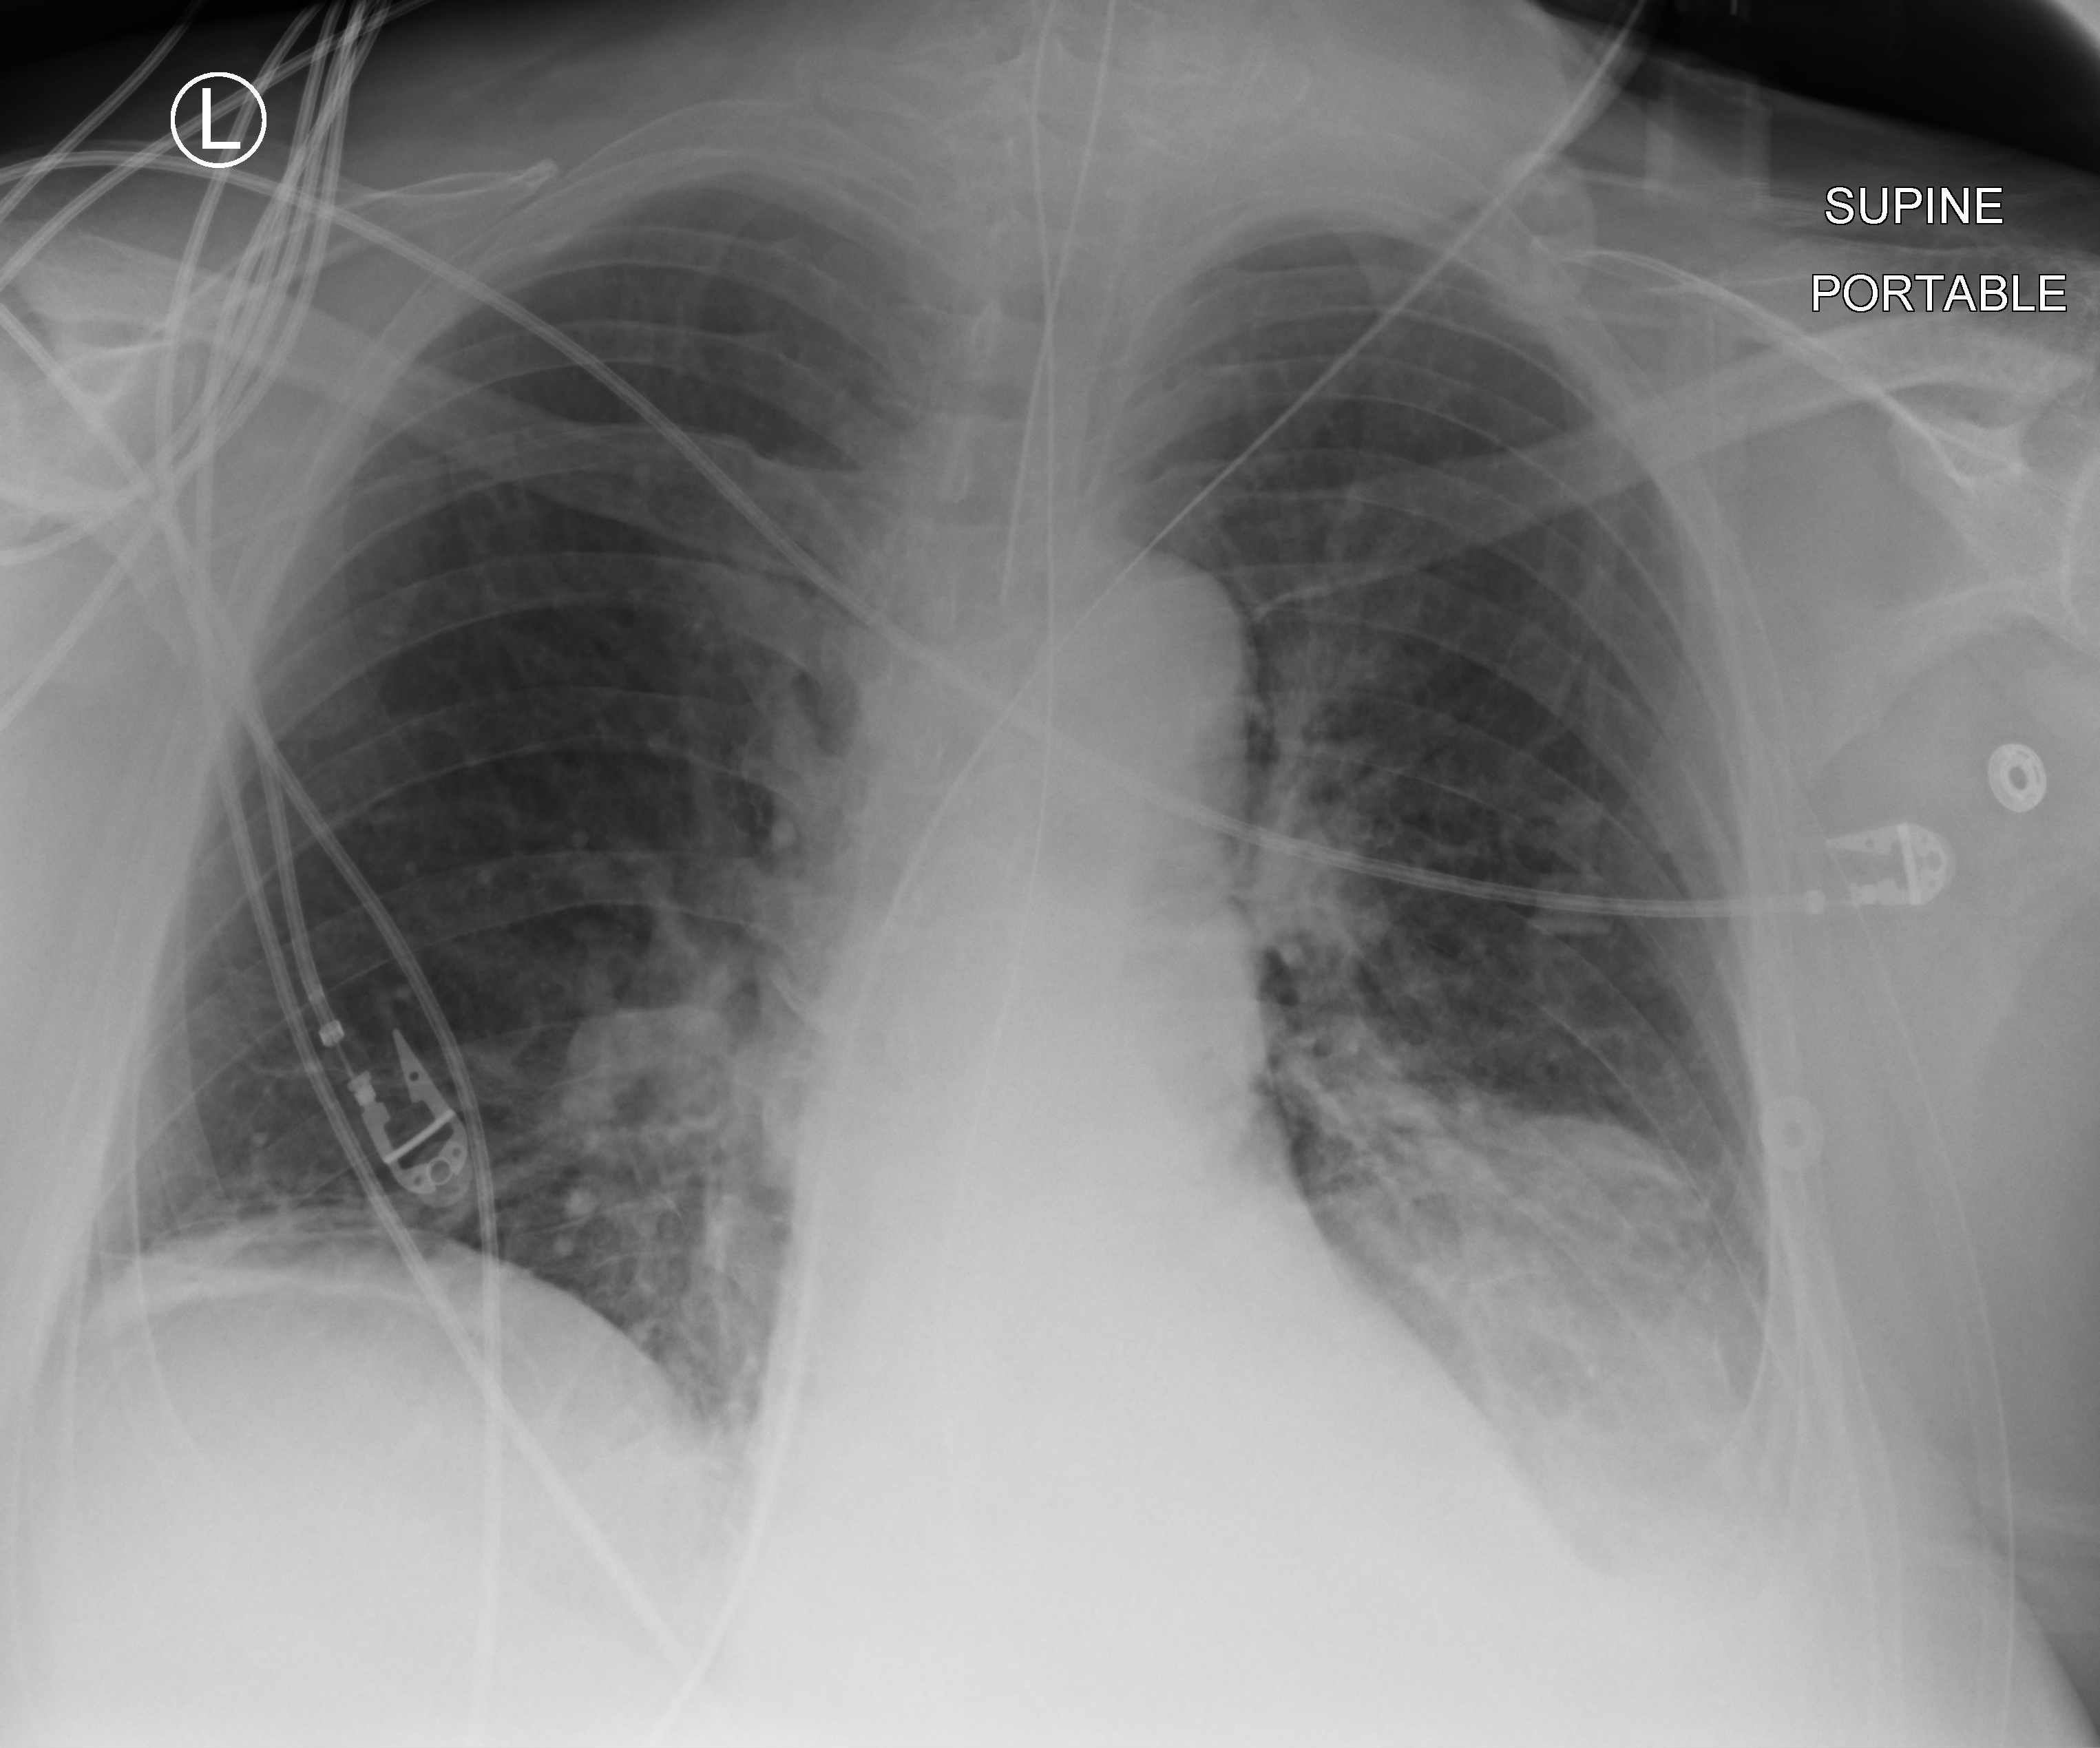
Portable chest radiograph; anteroposterior (AP) projection. Patient hospitalised with COVID-19; male, aged 60–74 years.
From the hospital-stay record, not from the radiograph (when in the stay this image was taken is not recorded):
- admitted to intensive care during this hospital stay: yes